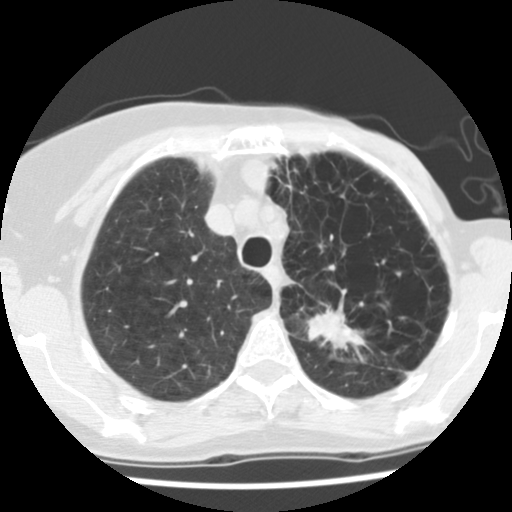
Low-dose screening chest CT, axial slice. Baseline screening round. Lung window (W 1500 / L -600 HU). Standard (soft-tissue) reconstruction kernel (STANDARD). 140 kVp. Slice 28 of 128 in the series. 512 × 512 image matrix, field of view 290 × 290 mm. Female participant, aged 67 years at enrolment. Current smoker at enrolment.
- Expert-annotated lung lesion, bounding box (x1, y1, x2, y2) in pixels: (295, 291, 385, 370).
- The screening reader recorded 2 non-calcified nodules or masses ≥4 mm on this exam (left upper lobe, left lower lobe); which of them this box marks is not recorded.
- Lung cancer was diagnosed 109 days after this screen: adenocarcinoma, NOS, left upper lobe, poorly differentiated (G3), stage IIB (AJCC 6th edition), 45 mm at pathology.